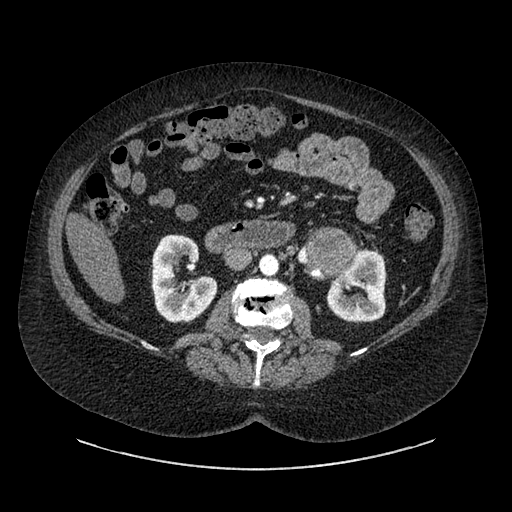
Contrast-enhanced abdominal CT, one axial slice; slice 494 of 769 in the series (ordered by position); reconstruction kernel SOFT; intravenous contrast given; soft-tissue window (W 400 / L 40 HU); 0.62 mm slice thickness; 512 × 512 image matrix. Female patient, age 61 years. Case-level facts recorded for this patient, not image findings: diagnosis: adrenocortical carcinoma; tumour side: left adrenal; tumour size at pathology: 13 cm; Ki-67 index: 79 %; stage (as recorded): 2.
Annotated regions visible in this slice (semi-automatic segmentation, software-assisted and operator-edited):
- mass: bounding box (x1, y1, x2, y2) in pixels: (313, 232, 353, 273)